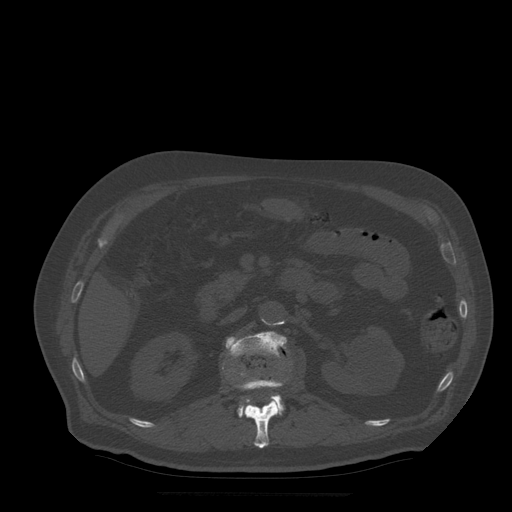
CT including the spine, one axial slice. Slice 185 of 522 in the series (ordered by position). Bone window (W 1800 / L 400 HU). 512 × 512 image matrix. Patient age 72 years. From the clinical record (not read from this slice): primary cancer: prostate.
Outlined on this slice (semi-automatically segmented with operator editing):
- L1 vertebra: bounding box <236,372,286,449> (left, top, right, bottom; pixels)
- L2 vertebra: <226,331,288,417>